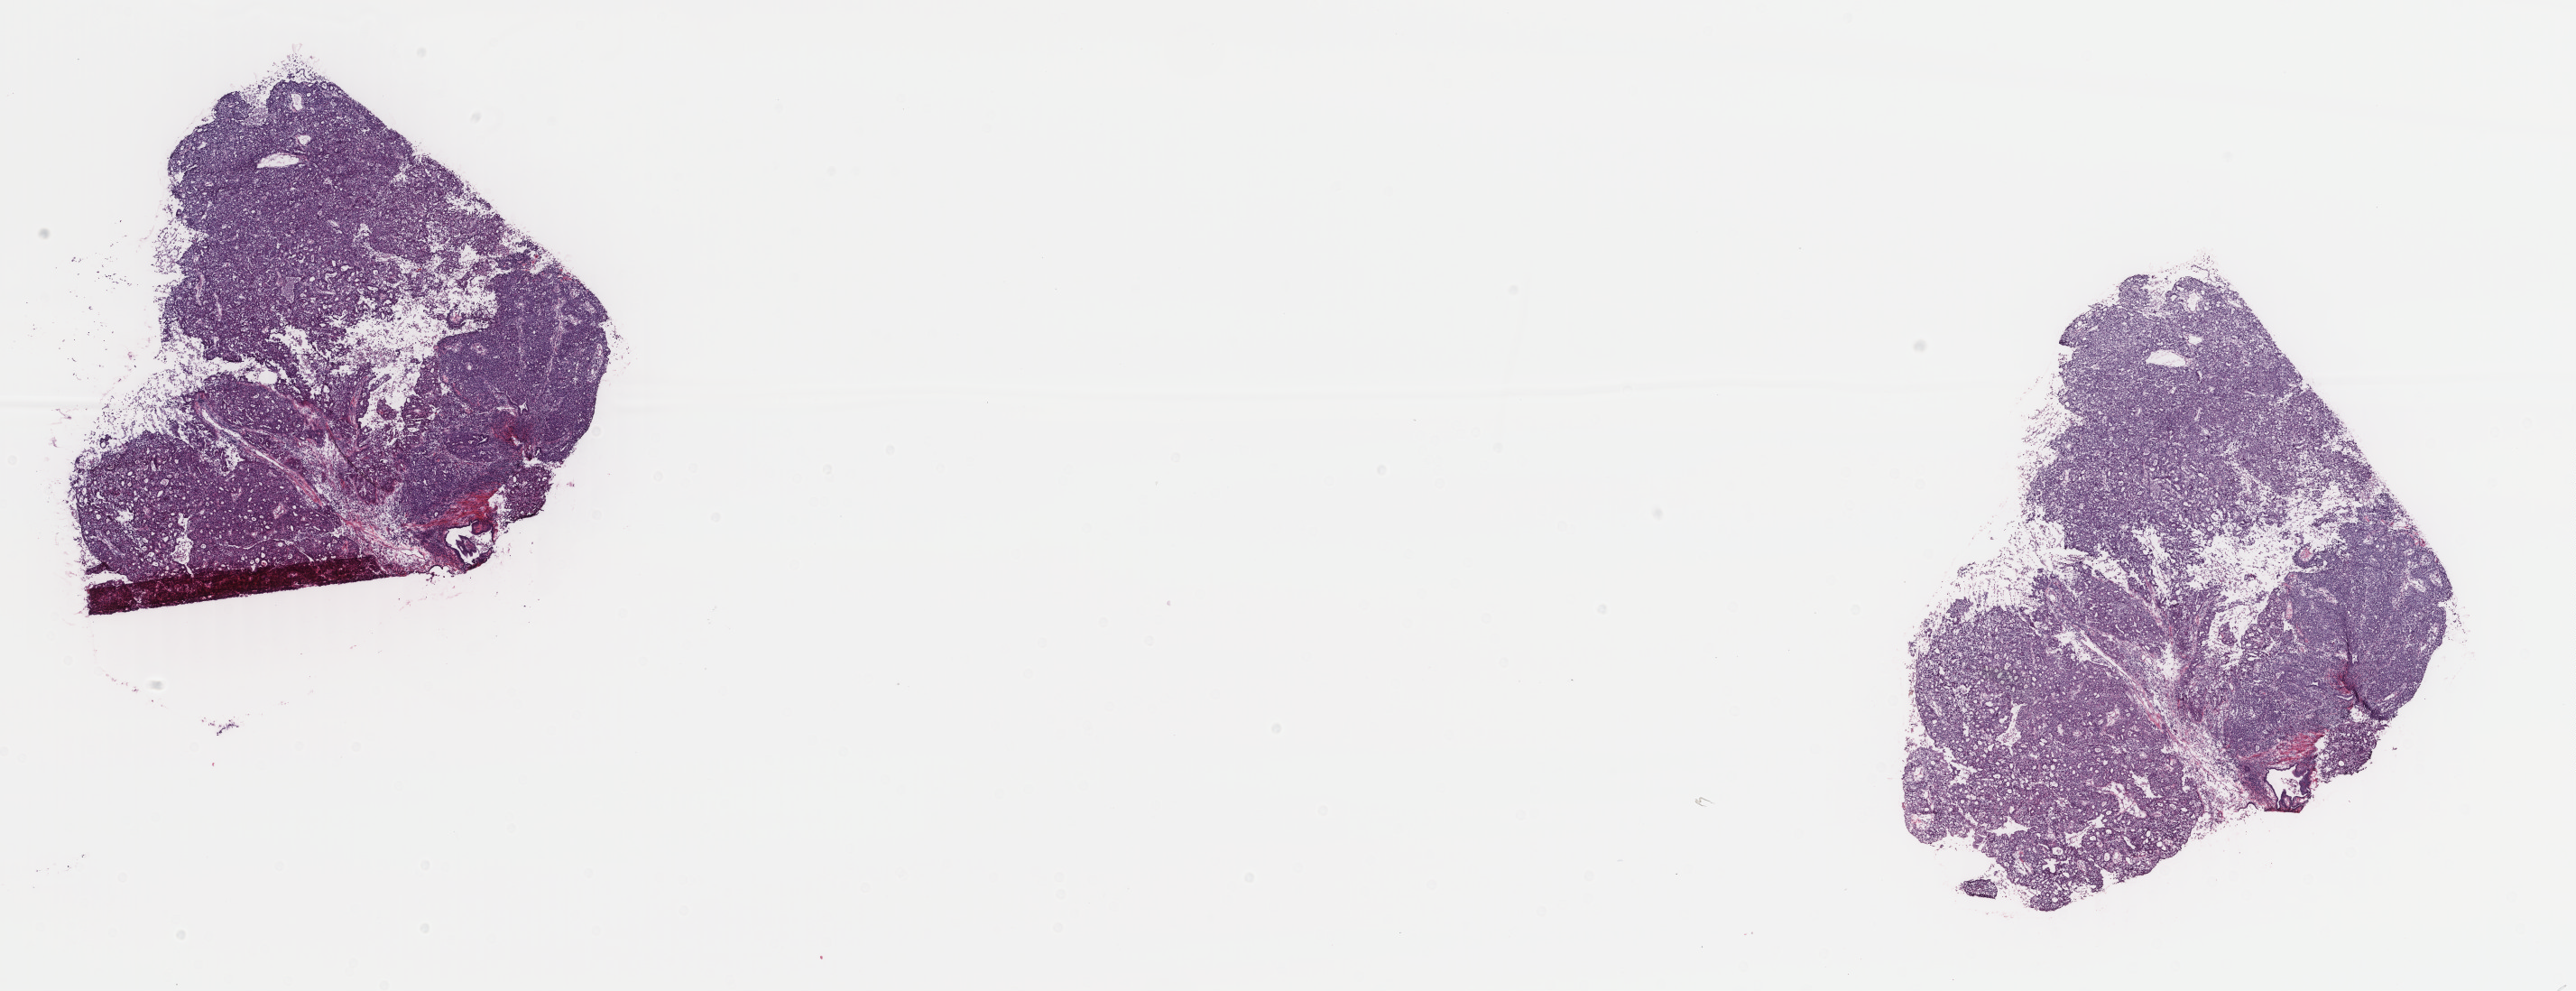
H&E whole-slide image — low-resolution overview of the scanned area, about 22.7 x 8.7 mm (slide scanned at 40x); frozen section from the top of the tissue portion; sample: primary tumour, uterus. Female patient. Composition of this section per pathologist review: tumour cells 93%, tumour nuclei 95%.
Histologic diagnosis: Endometrioid adenocarcinoma, NOS (endometrium).